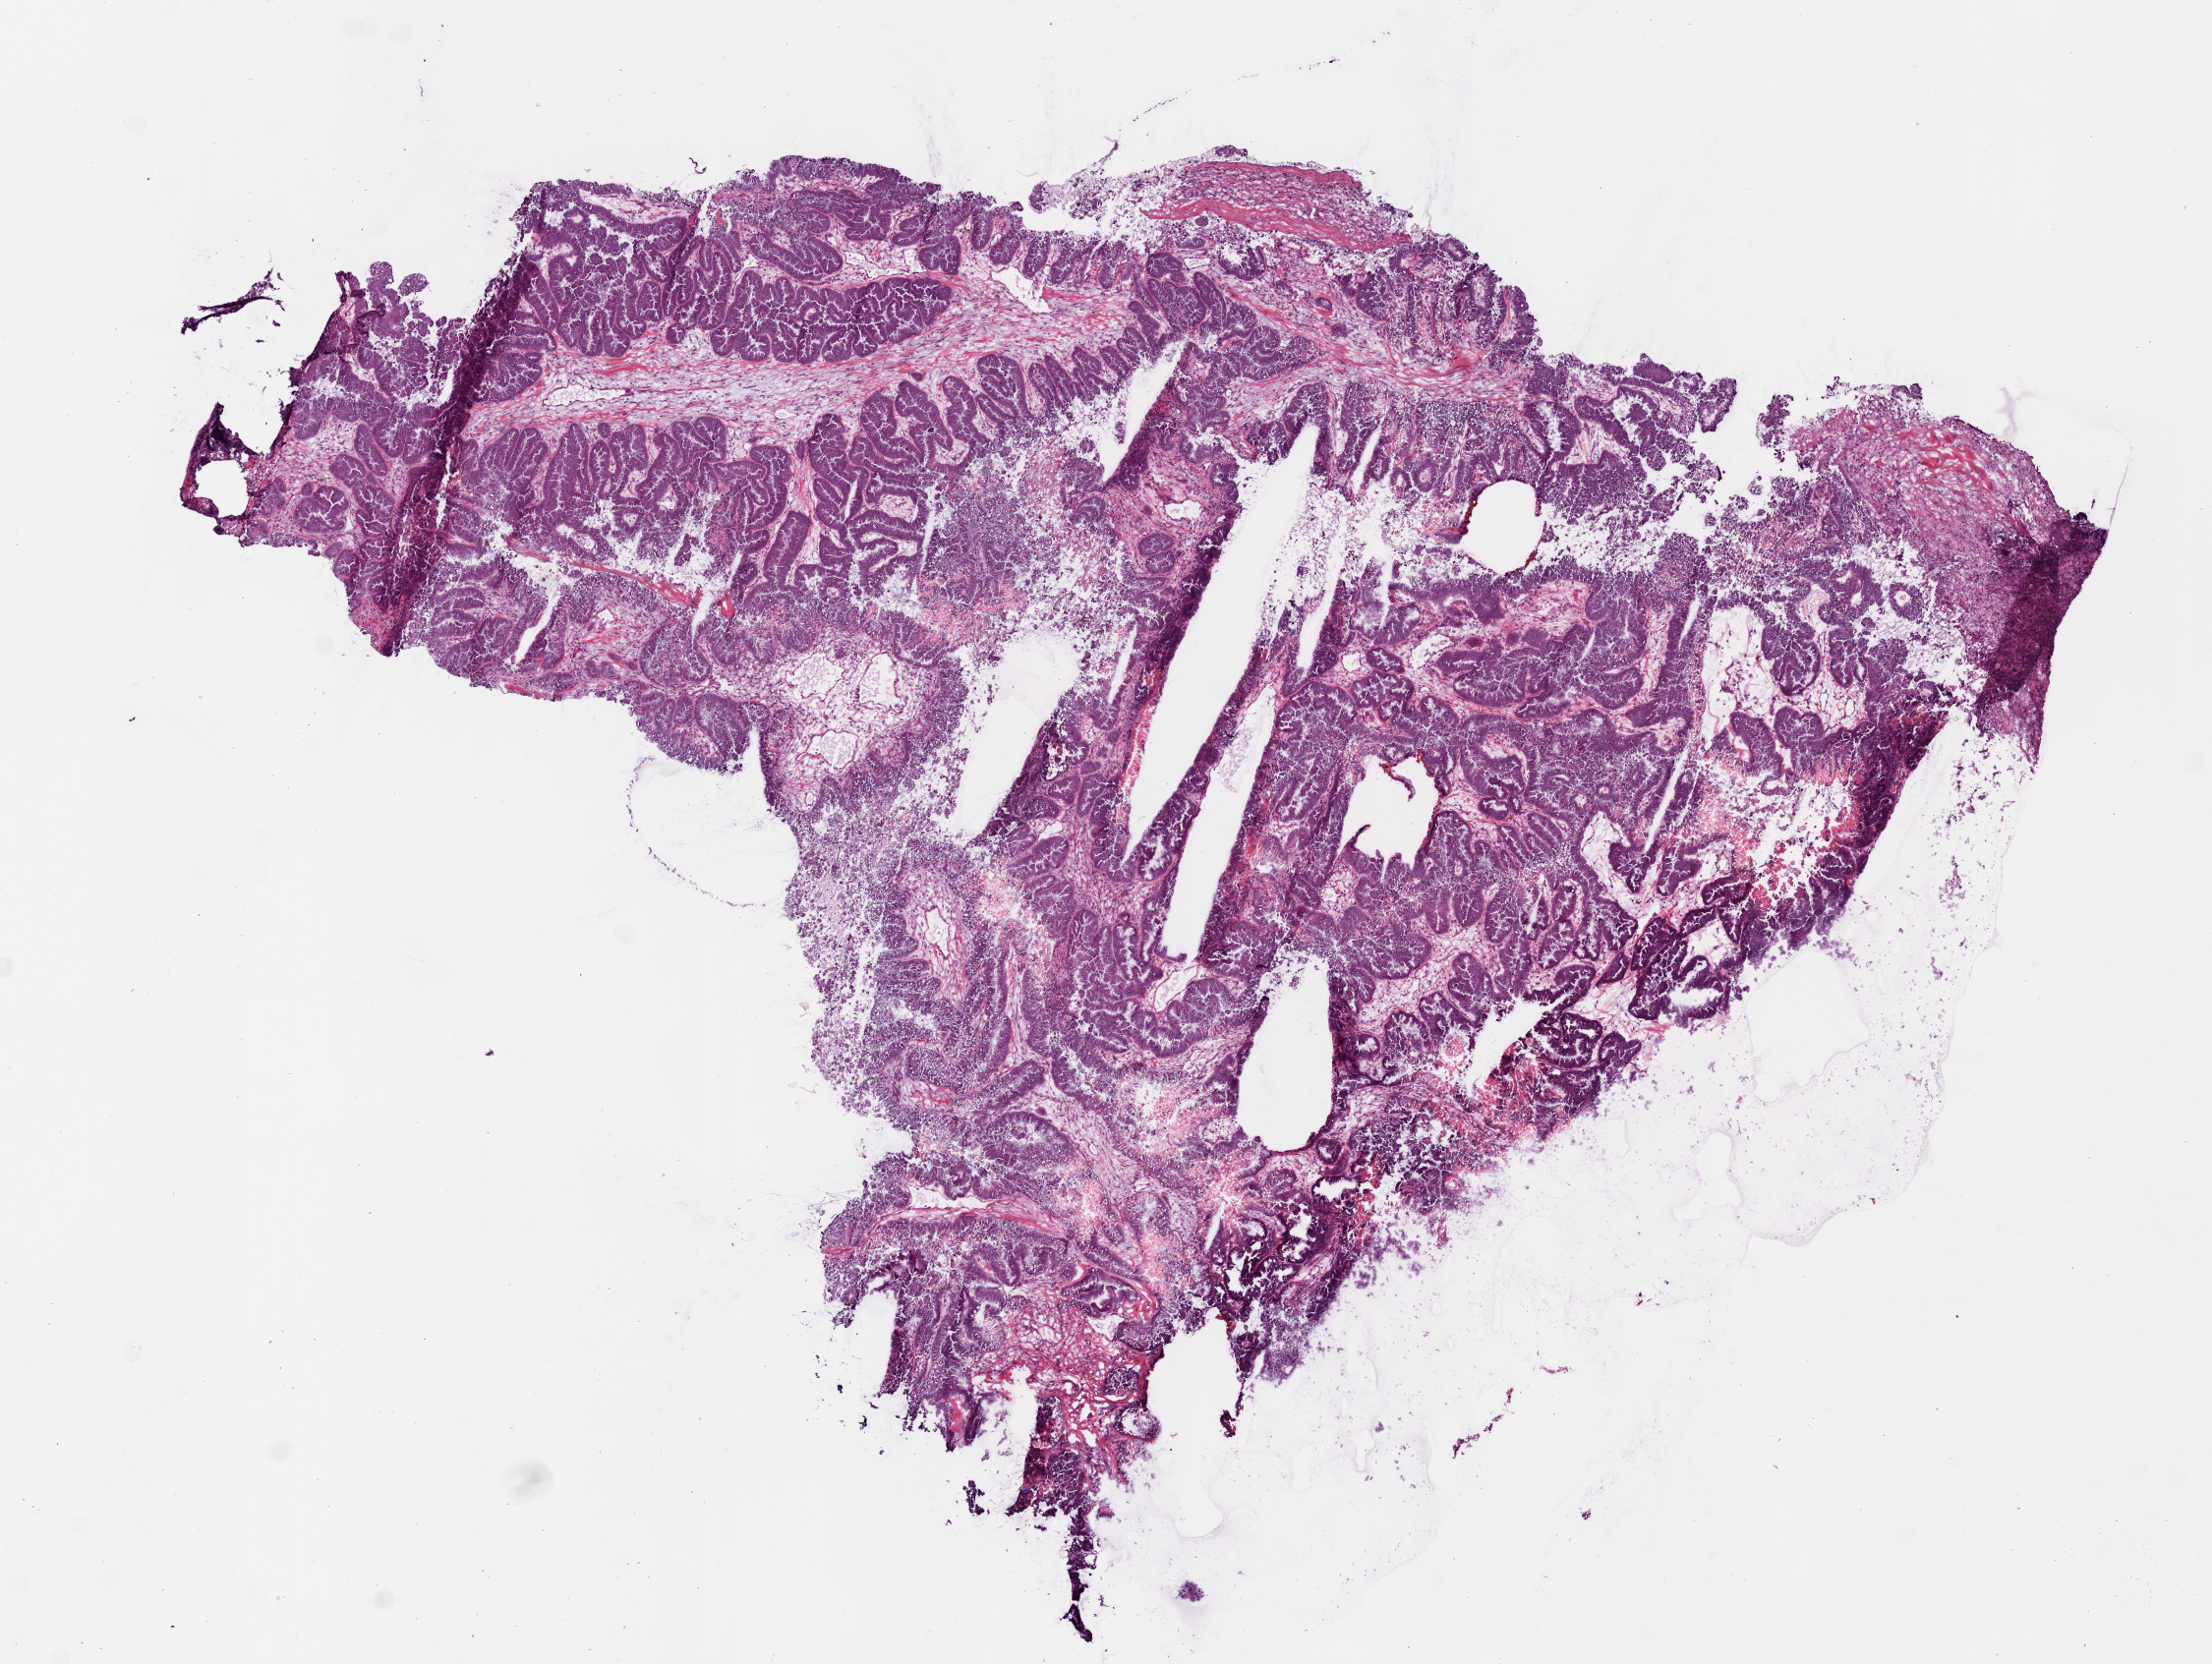
Whole-slide histology image, H&E-stained — shown as a low-resolution overview of the whole scanned area (about 9.0 x 6.8 mm, from a 20x scan), frozen section from the top of the tissue portion, primary tumour sample from the lung. Male, age 81 years at initial diagnosis. Pathologist review of this section (percent, as recorded): tumour cells 98%, tumour nuclei 85%, normal cells 0%, stromal cells 0%, necrosis 2%. Infiltration values recorded for this section: monocyte infiltration 2%.
• pathologic diagnosis: Papillary adenocarcinoma, NOS
• AJCC pathologic stage: IV (7th edition)